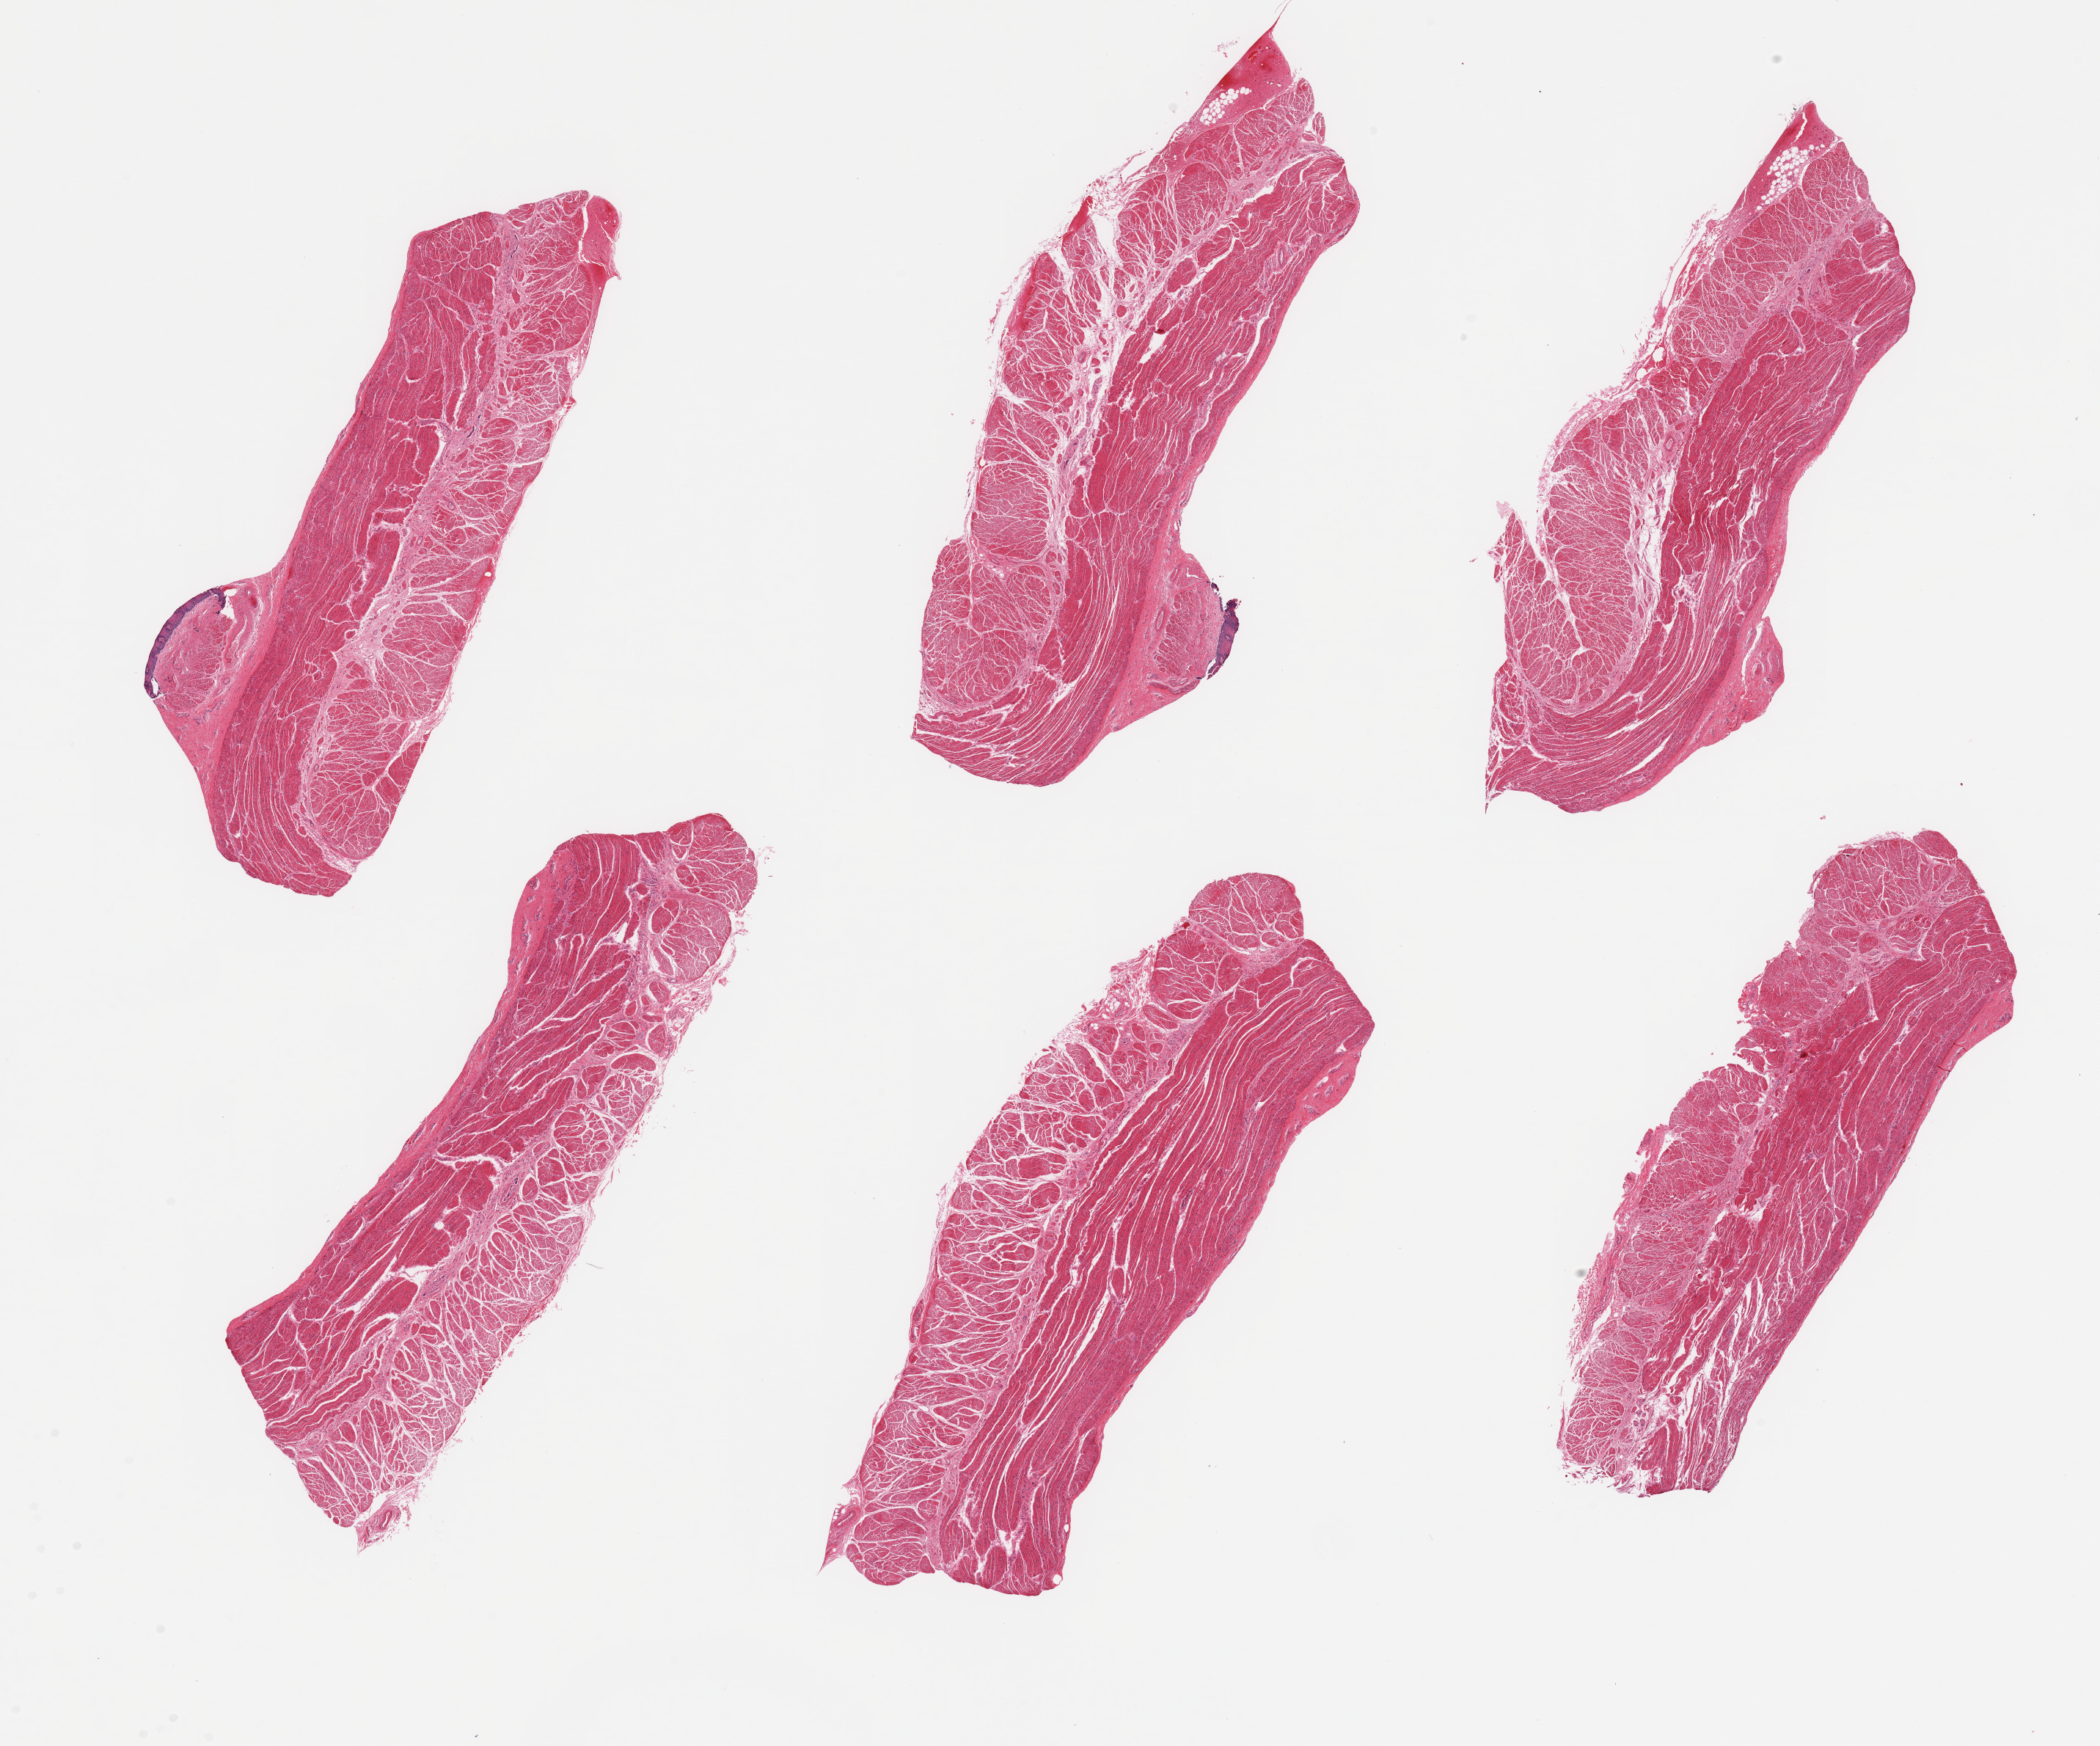
Whole-slide image, hematoxylin and eosin (H&E) stain — a low-resolution overview of the entire scanned area, about 22.6 x 18.8 mm (from a 20x scan); PAXgene-fixed, paraffin-embedded tissue; sampled site (target tissue): esophageal muscle; tissue donor sample. Donor sex: male.
- review note (as recorded): 6 pieces, confirmed target muscularis